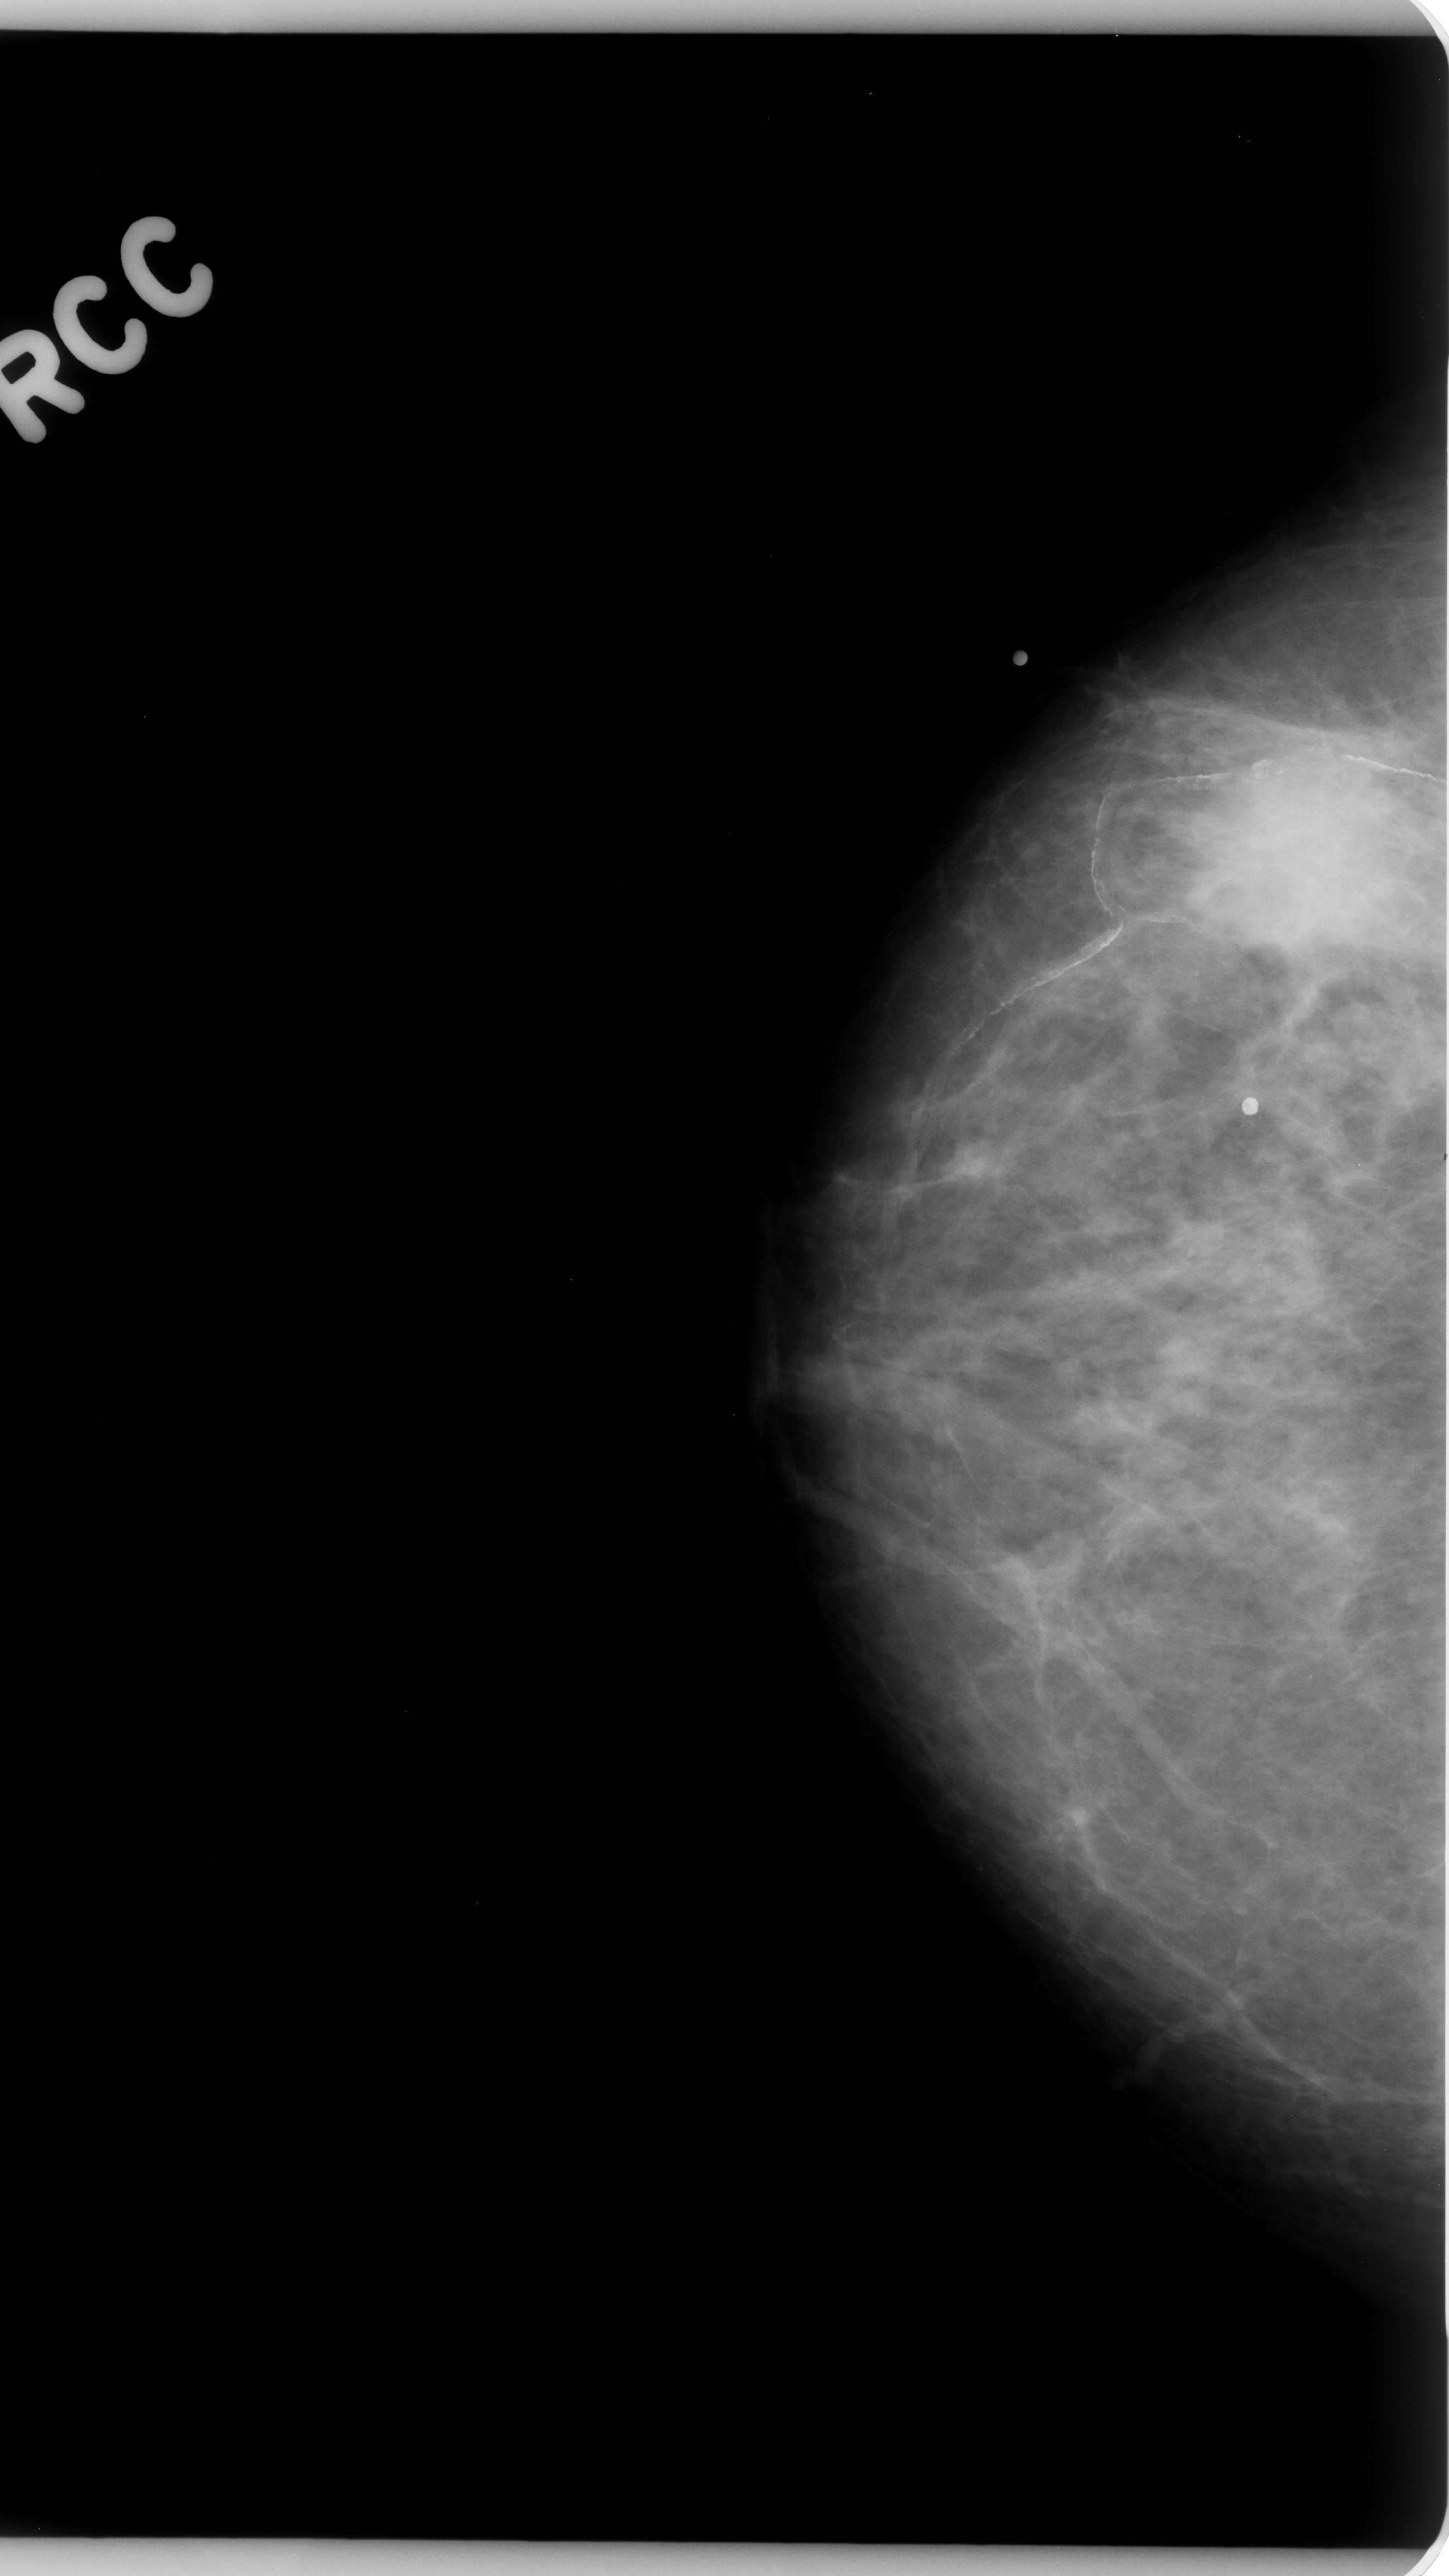
Digitized screen-film mammogram. Right breast. Craniocaudal (CC) view. 1449 × 2576 image matrix.
Expert-marked regions of interest on this film, with their recorded descriptors:
- mass, shape round, margins ill defined; BI-RADS assessment category 5; subtlety rating 5 on a 1 (subtle) to 5 (obvious) scale; pathology (as recorded): malignant: bounding box (x1, y1, x2, y2) in pixels: (1196, 722, 1407, 1046)